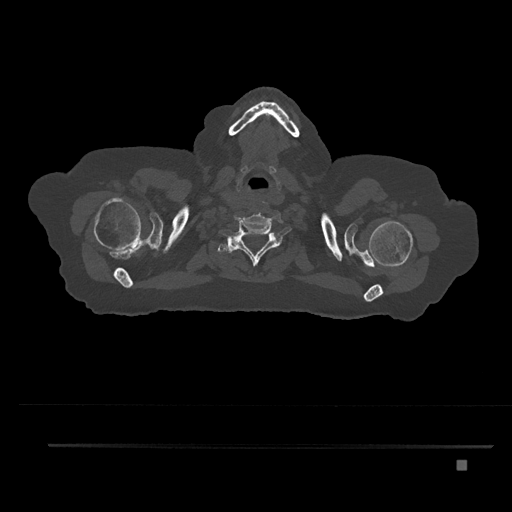
CT including the spine, one axial slice; slice 723 of 797 in the series (ordered by position); 120 kVp; bone window (W 1800 / L 400 HU); 0.5 mm slice thickness; 512 × 512 image matrix, field of view 437 × 437 mm. Patient: female, 76 years. Case-level facts recorded for this patient, not image findings: primary cancer: lung; vertebrae with lytic lesions (as recorded): T11, L3.
Outlined on this slice (semi-automatically segmented with operator editing):
- T1 vertebra: bounding box [x1, y1, x2, y2] px = [224, 240, 253, 256]